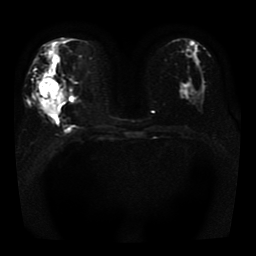
Breast MRI, one axial slice. Position 20 of 41 along the scan axis. Diffusion-weighted series; image 2 of 4 stored at this slice position (different b-values; order by instance number). 1.5 T. 5 mm slice thickness. 256 × 256 image matrix, field of view 330 × 330 mm. Female patient.
Outlined on this slice (expert manual segmentation):
- tumour on diffusion-weighted imaging: bounding box (x1, y1, x2, y2) in pixels: (38, 78, 61, 113)